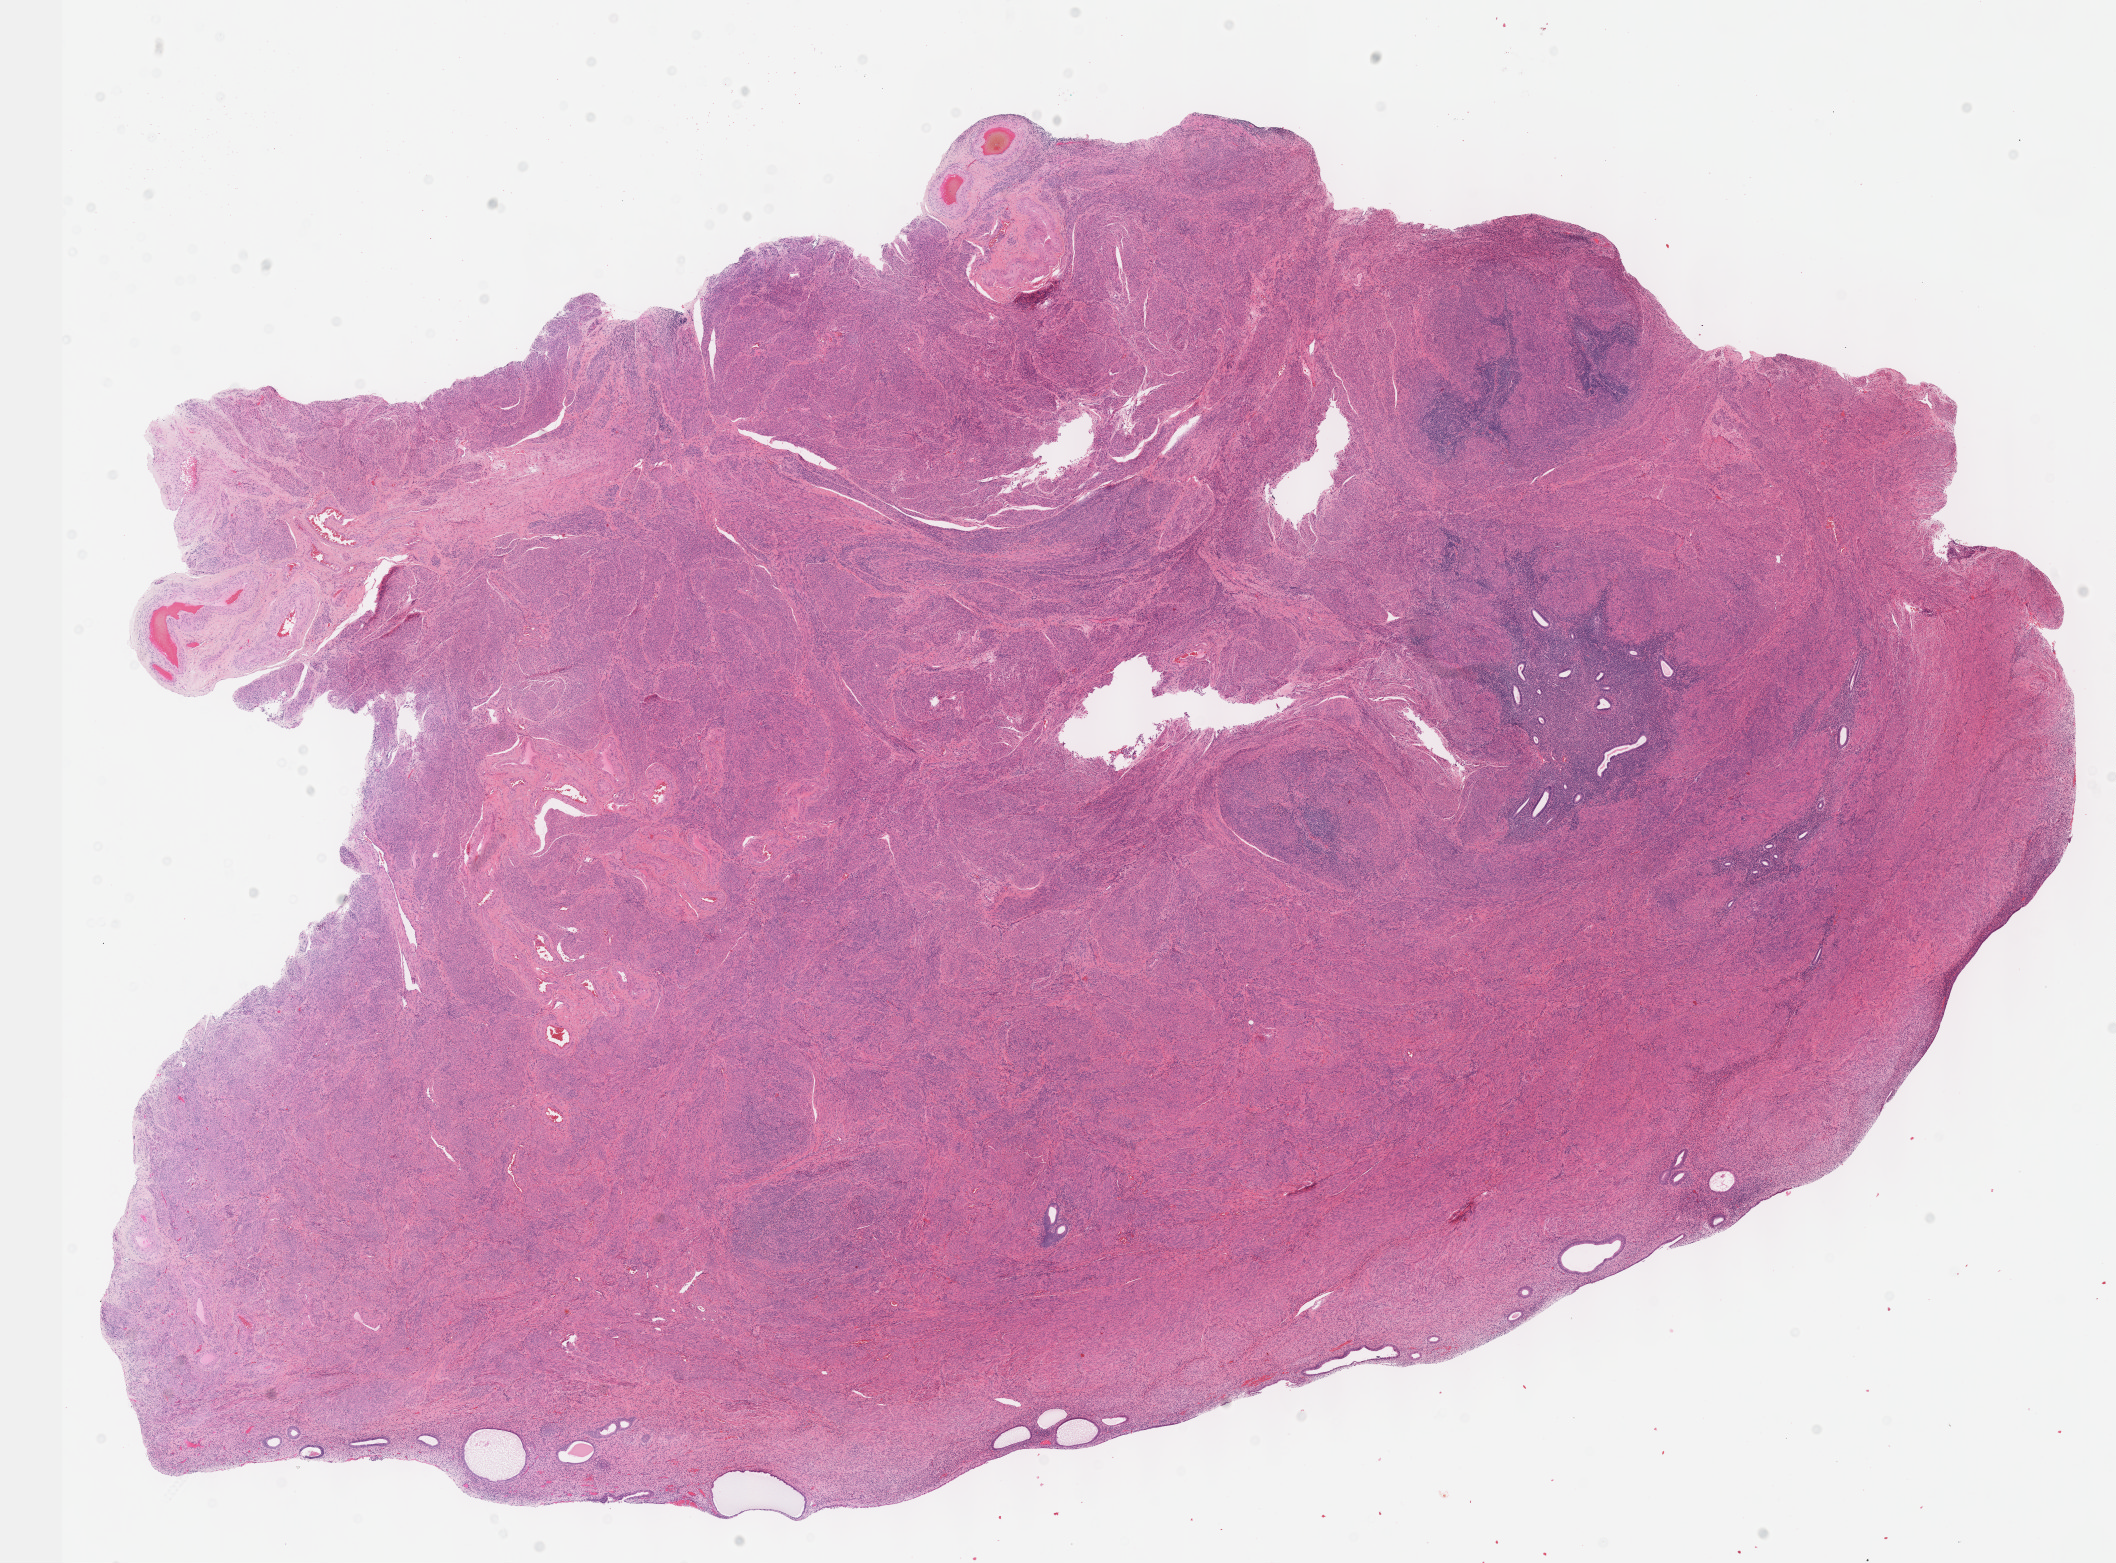
H&E whole-slide image — low-resolution overview of the scanned area, about 17.1 x 12.6 mm, formalin-fixed paraffin-embedded (FFPE) diagnostic section, uterus, primary tumour sample. Female, age 70 years at initial diagnosis. Histologic grade: G2 (moderately differentiated).
• histologic diagnosis: Endometrioid adenocarcinoma, NOS (endometrium)
• FIGO stage: I